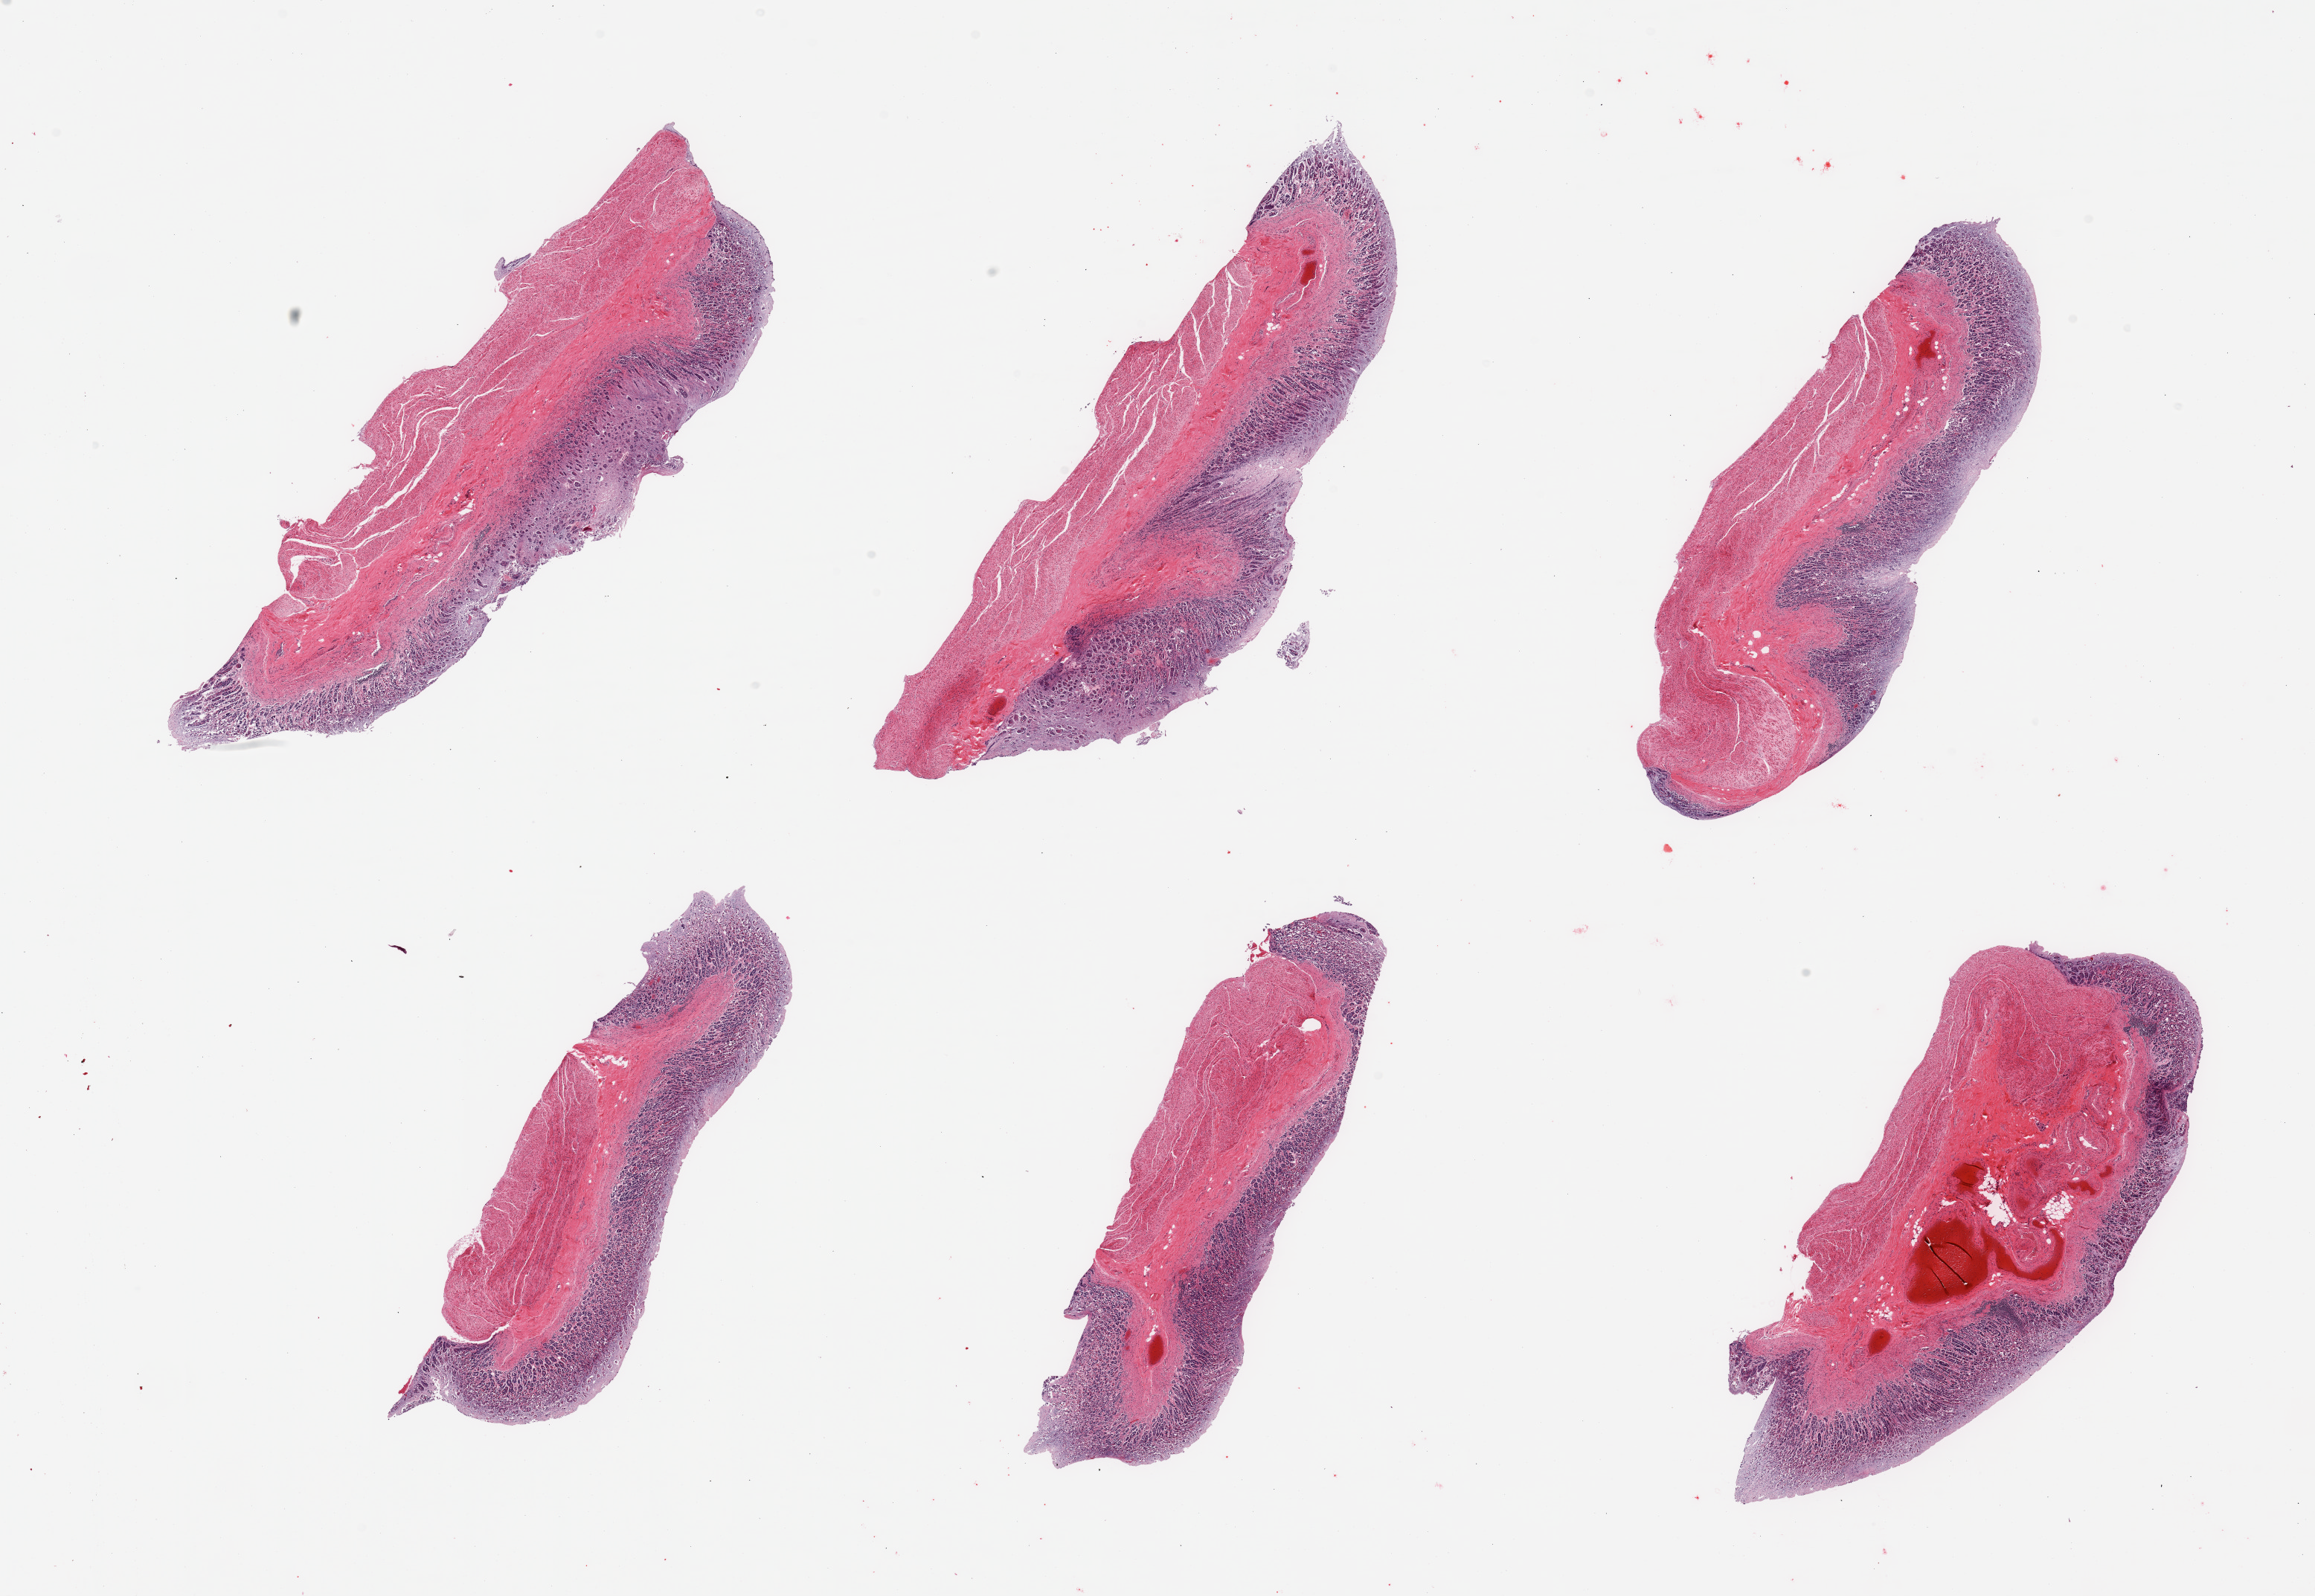
Whole-slide image, hematoxylin and eosin (H&E) stain — whole scanned area (about 24.6 x 17.0 mm, slide scanned at 20x) shown as a low-resolution overview; PAXgene-fixed, paraffin-embedded tissue; section of stomach (target tissue); donor tissue sample. Donor sex: female.
• pathologist's review note for this sample: 6 pieces; mucosa severely autolyzed, muscularis moderately autolyzed